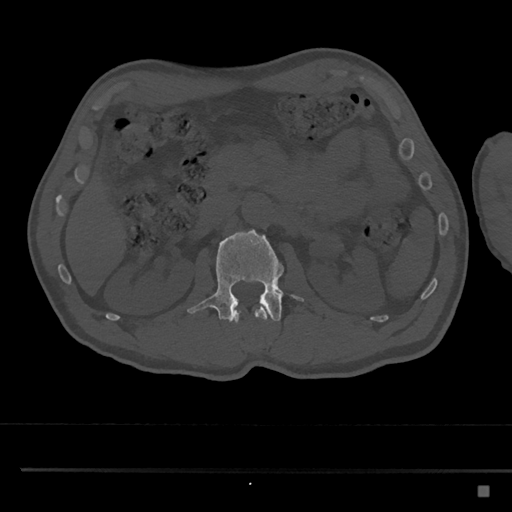
CT including the spine, one axial slice. Bone window (W 1800 / L 400 HU). 0.5 mm slice thickness. 512 × 512 image matrix, field of view 391 × 391 mm. Male patient, age 59 years. From the clinical record (not read from this slice): primary cancer: prostate.
Structures marked on this image (semi-automatic segmentation, software-assisted and operator-edited):
- L1 vertebra: bounding box [x1, y1, x2, y2] px = [232, 307, 269, 322]
- L2 vertebra: [187, 229, 305, 322]